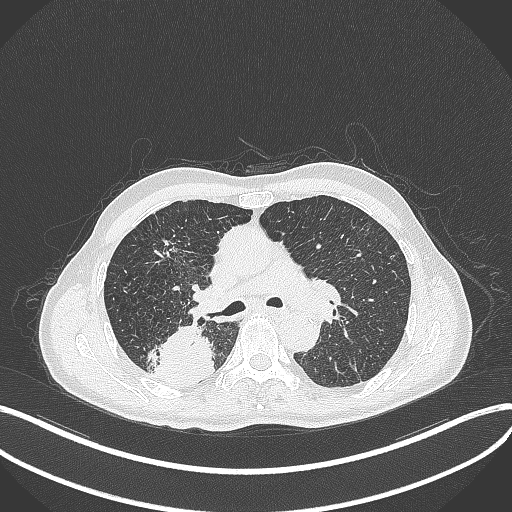
Chest CT, one axial slice; position 286 of 428 along the scan axis; reconstruction kernel B70f; lung window (W 1500 / L -600 HU); 1 mm slice thickness; 512 × 512 image matrix, field of view 400 × 400 mm. Patient: male, 79 years. Case-level facts recorded for this patient, not image findings: clinical TNM (as recorded): T3 N0 M0.
Outlined on this slice (rectangle marked by the reading radiologist):
- lung tumour (recorded histology: adenocarcinoma): bounding box <153,324,215,388> (left, top, right, bottom; pixels)